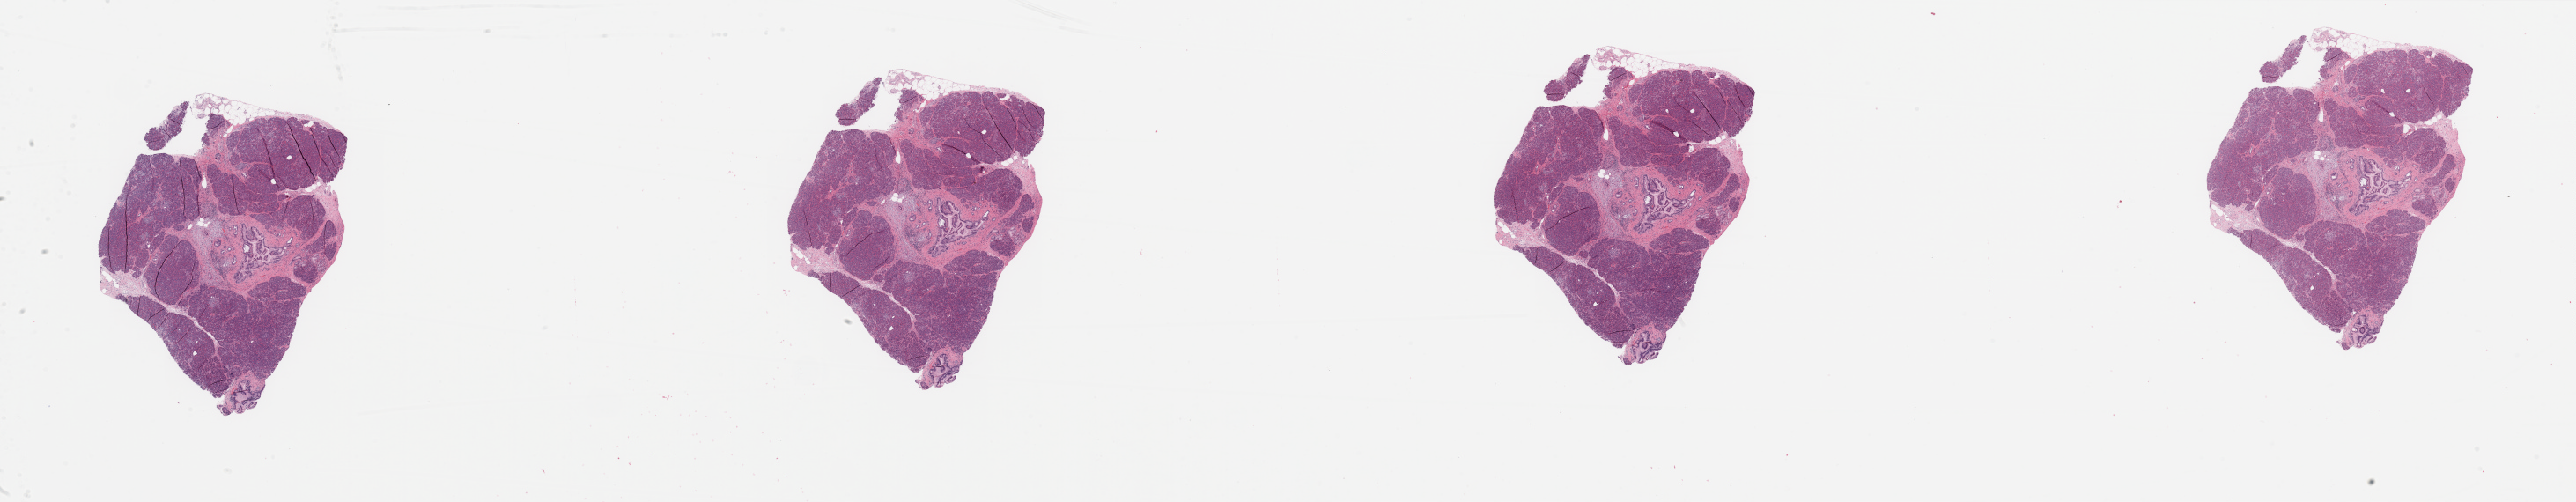
Whole-slide histology image, H&E-stained, a low-resolution overview of the entire scanned area, about 46.3 x 9.0 mm (from a 20x scan); pancreas, normal (non-tumour) tissue. Patient: female, age 69 years.
This section: normal (non-tumour) tissue from the same patient. Patient diagnosis: Infiltrating duct carcinoma, NOS.